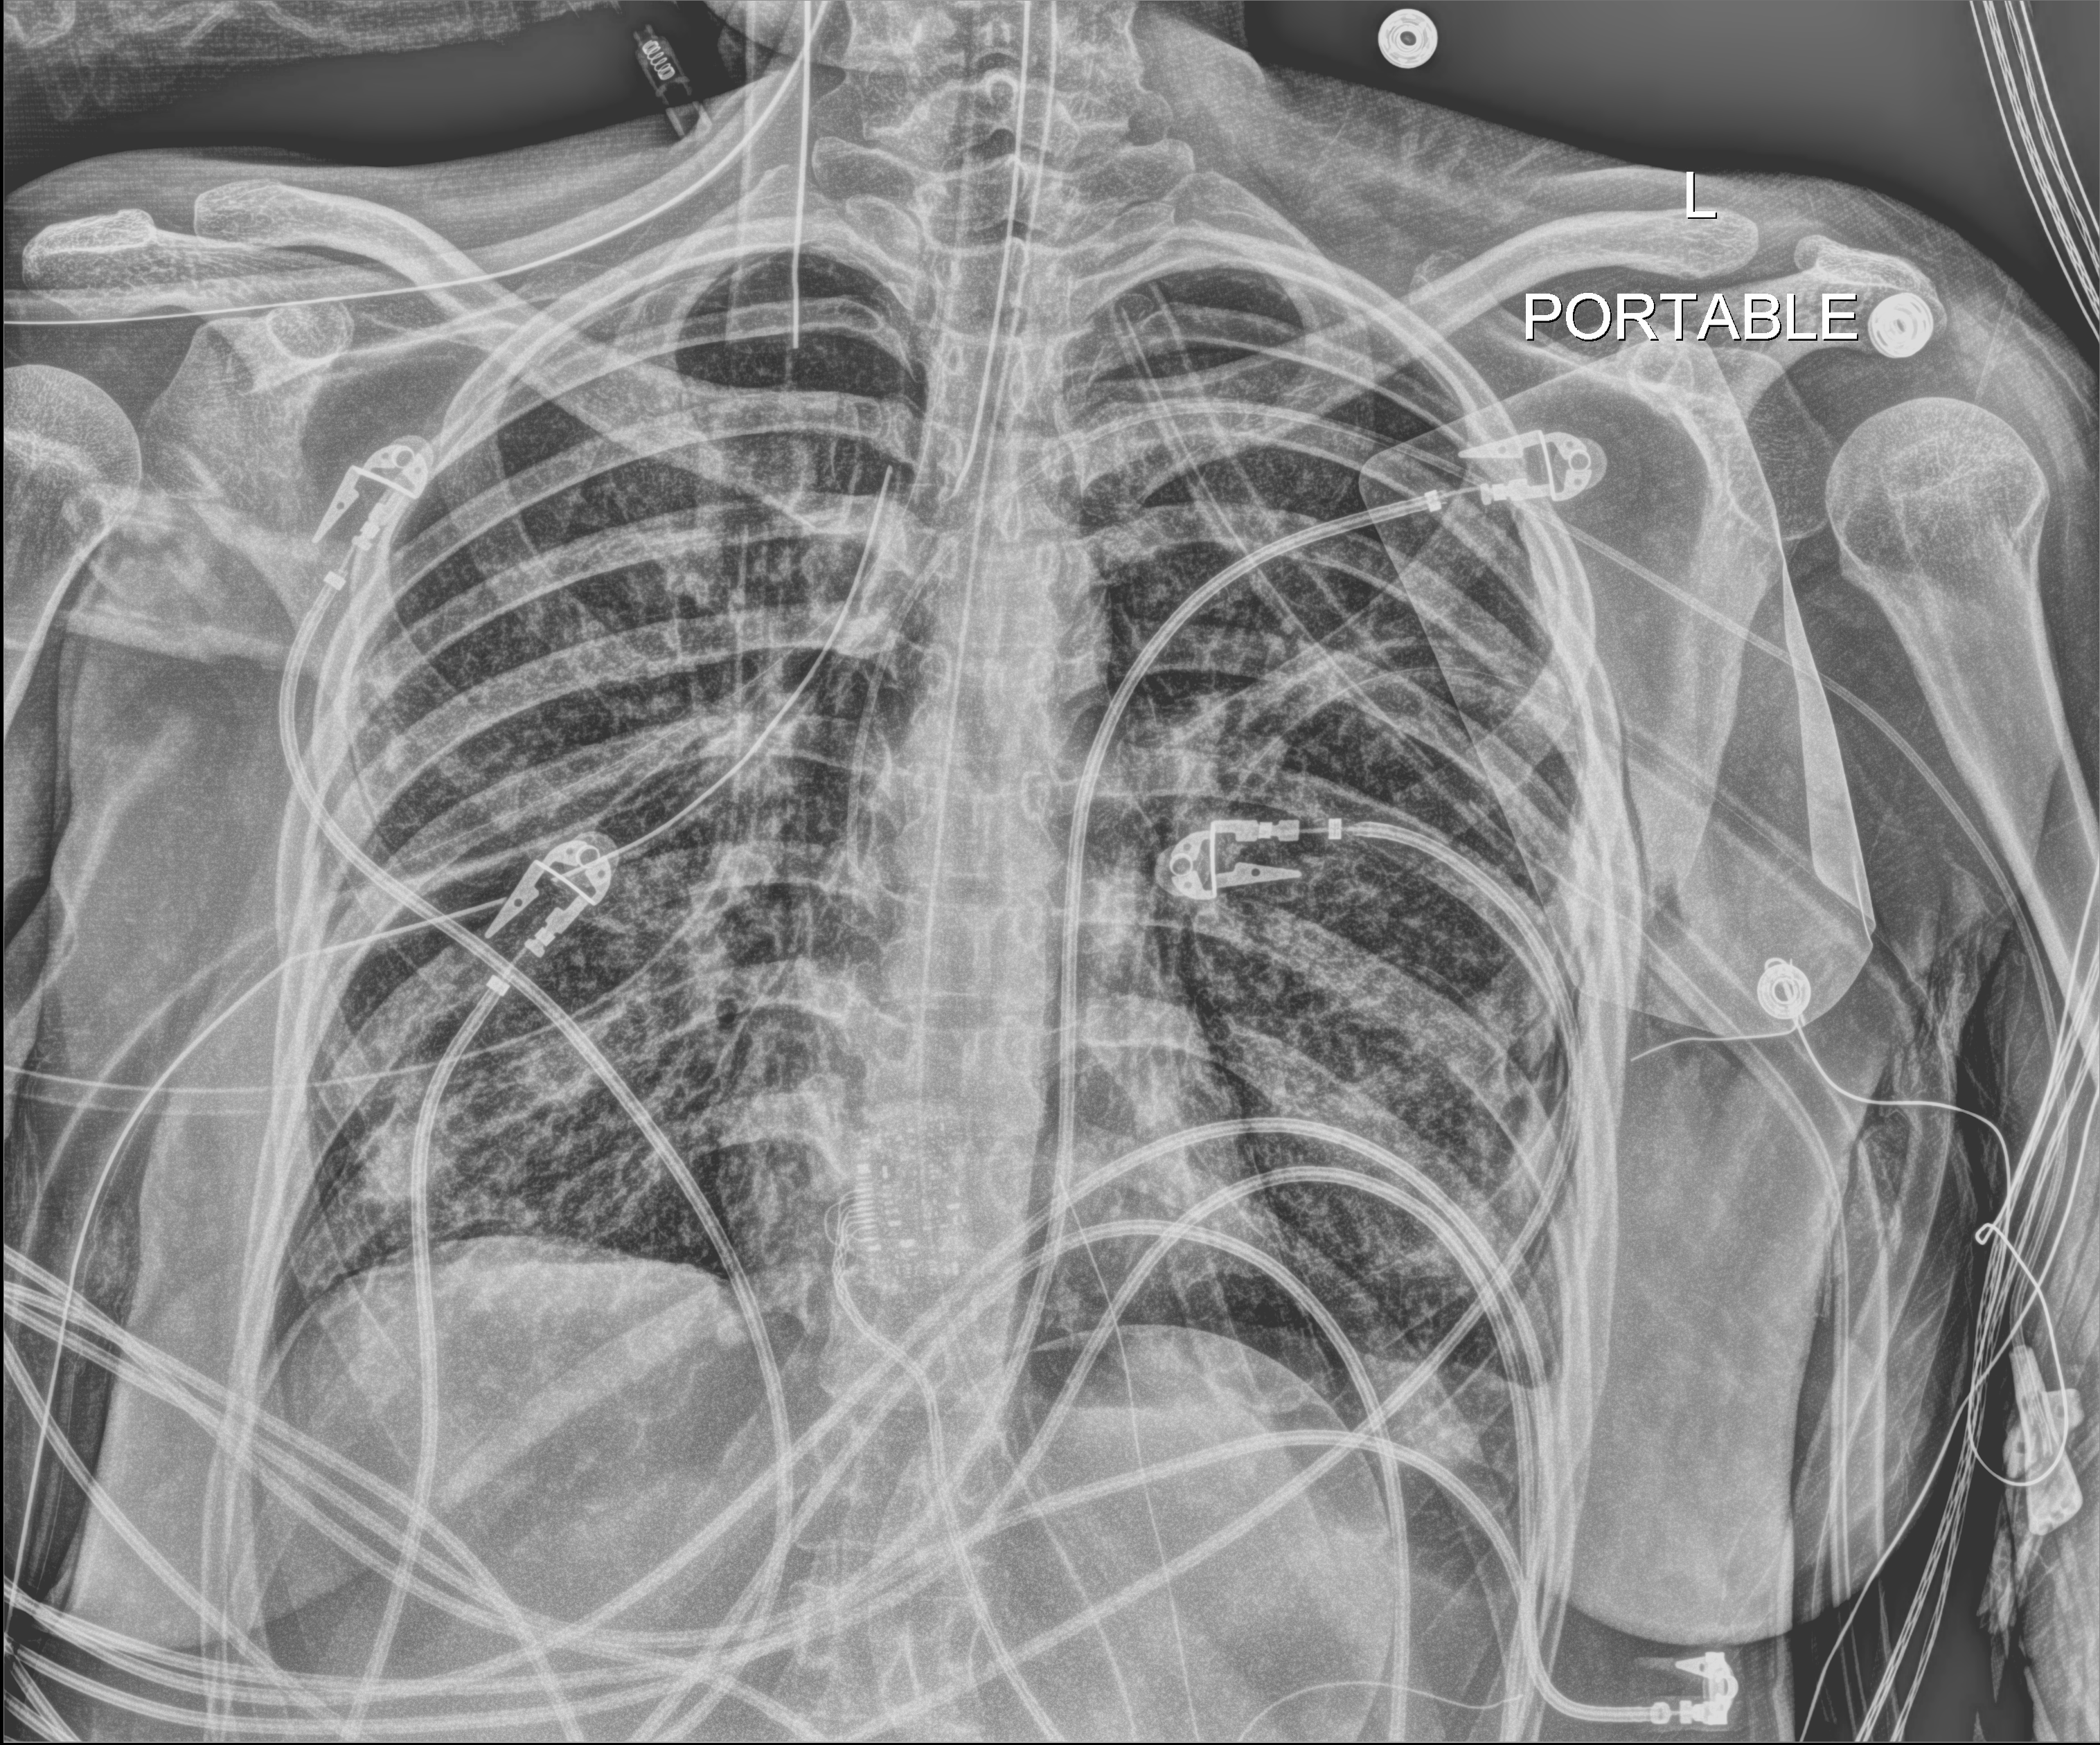
Bedside chest radiograph (digital radiography), anteroposterior (AP) projection. Patient hospitalised with COVID-19, aged 18–59 years.
Hospital-stay facts (about this admission, not read from this image; timing relative to this image not recorded): length of hospital stay: 30 days; mechanically ventilated during this hospital stay: yes.